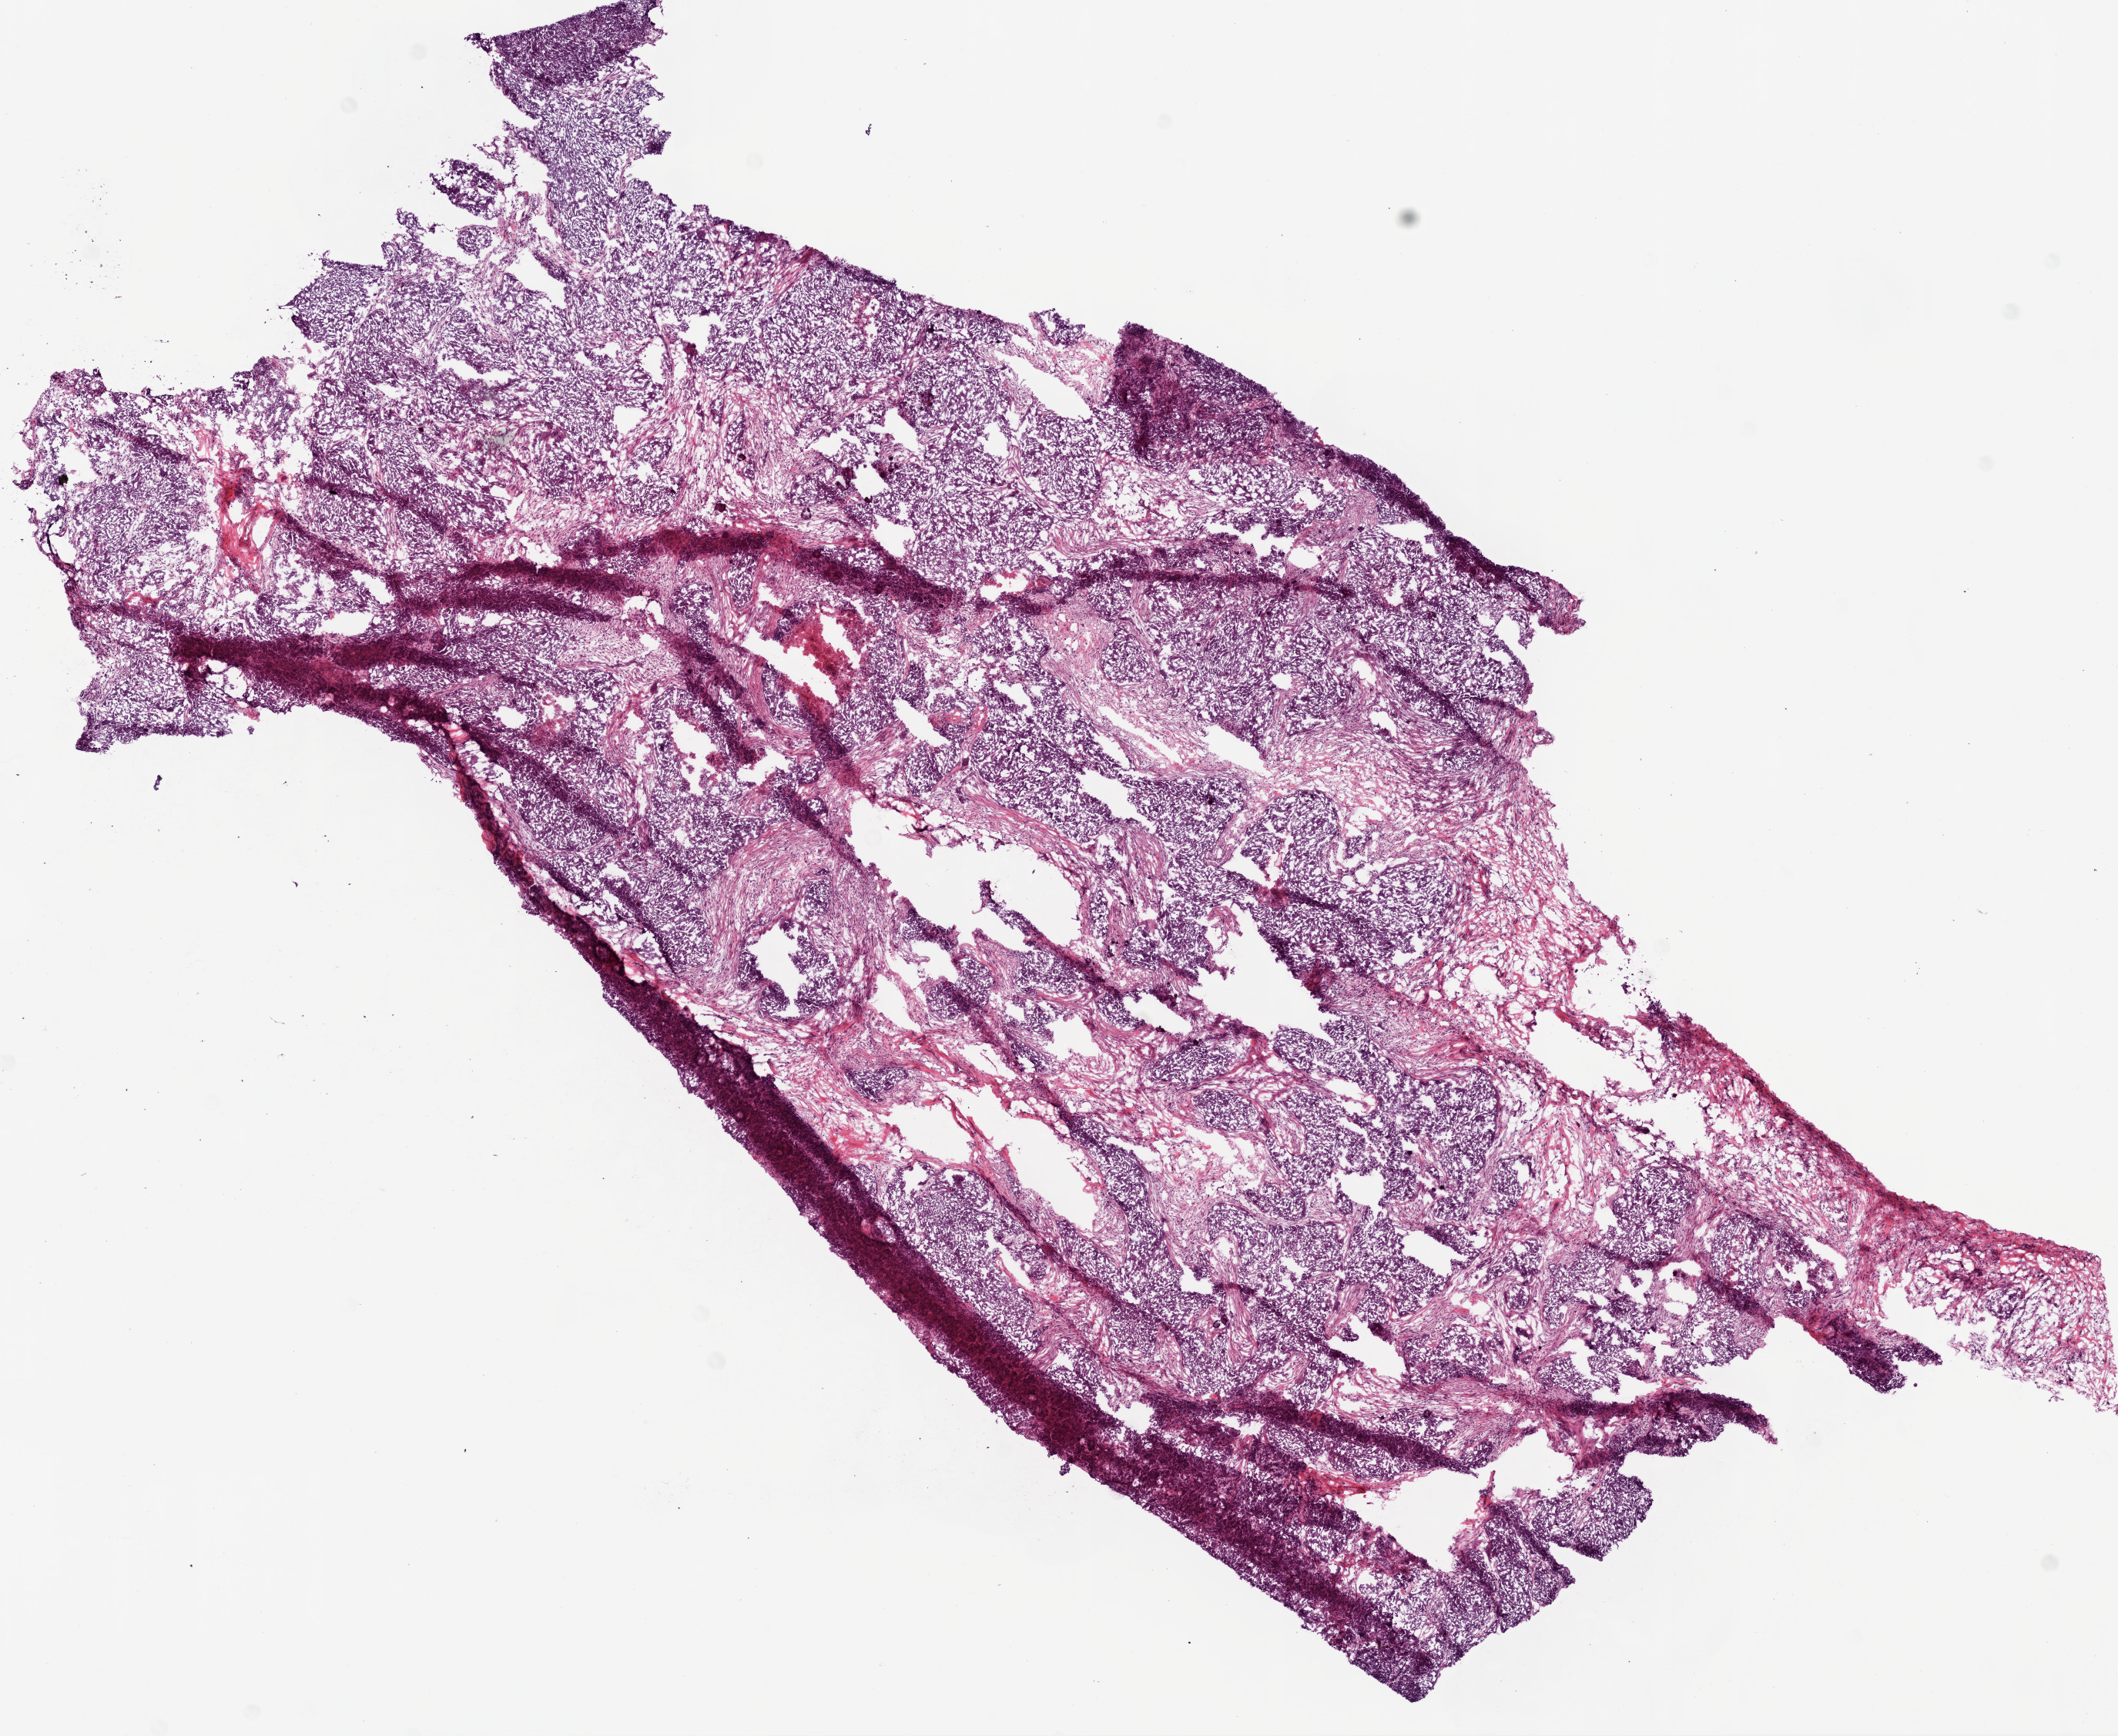
Whole-slide histology image, H&E, low-resolution overview of the scanned area, about 11.0 x 9.0 mm; frozen section; ovary, primary tumour sample. Female, age 67 years at initial diagnosis. Histologic grade: G3 (poorly differentiated). Slide review estimates, as recorded: tumour cells 85%, tumour nuclei 90%, normal cells 0%, stromal cells 10%, necrosis 5%.
Diagnosis: Serous cystadenocarcinoma, NOS. FIGO stage: IIIC.